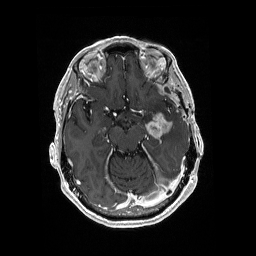
Brain MRI from a brain-tumour surgery series, one axial slice. Slice 114 of 176 in the series (ordered by position). T1-weighted post-contrast. 1 mm slice thickness. 256 × 256 image matrix, field of view 256 × 256 mm. From the clinical record (not read from this slice): histopathology: Glioblastoma; WHO grade: 4; IDH mutation: no; tumour location: Left Medial Temporal.
Outlined on this slice (outlined manually by an expert reader):
- tumour: box from (x=145, y=112) to (x=174, y=138) px